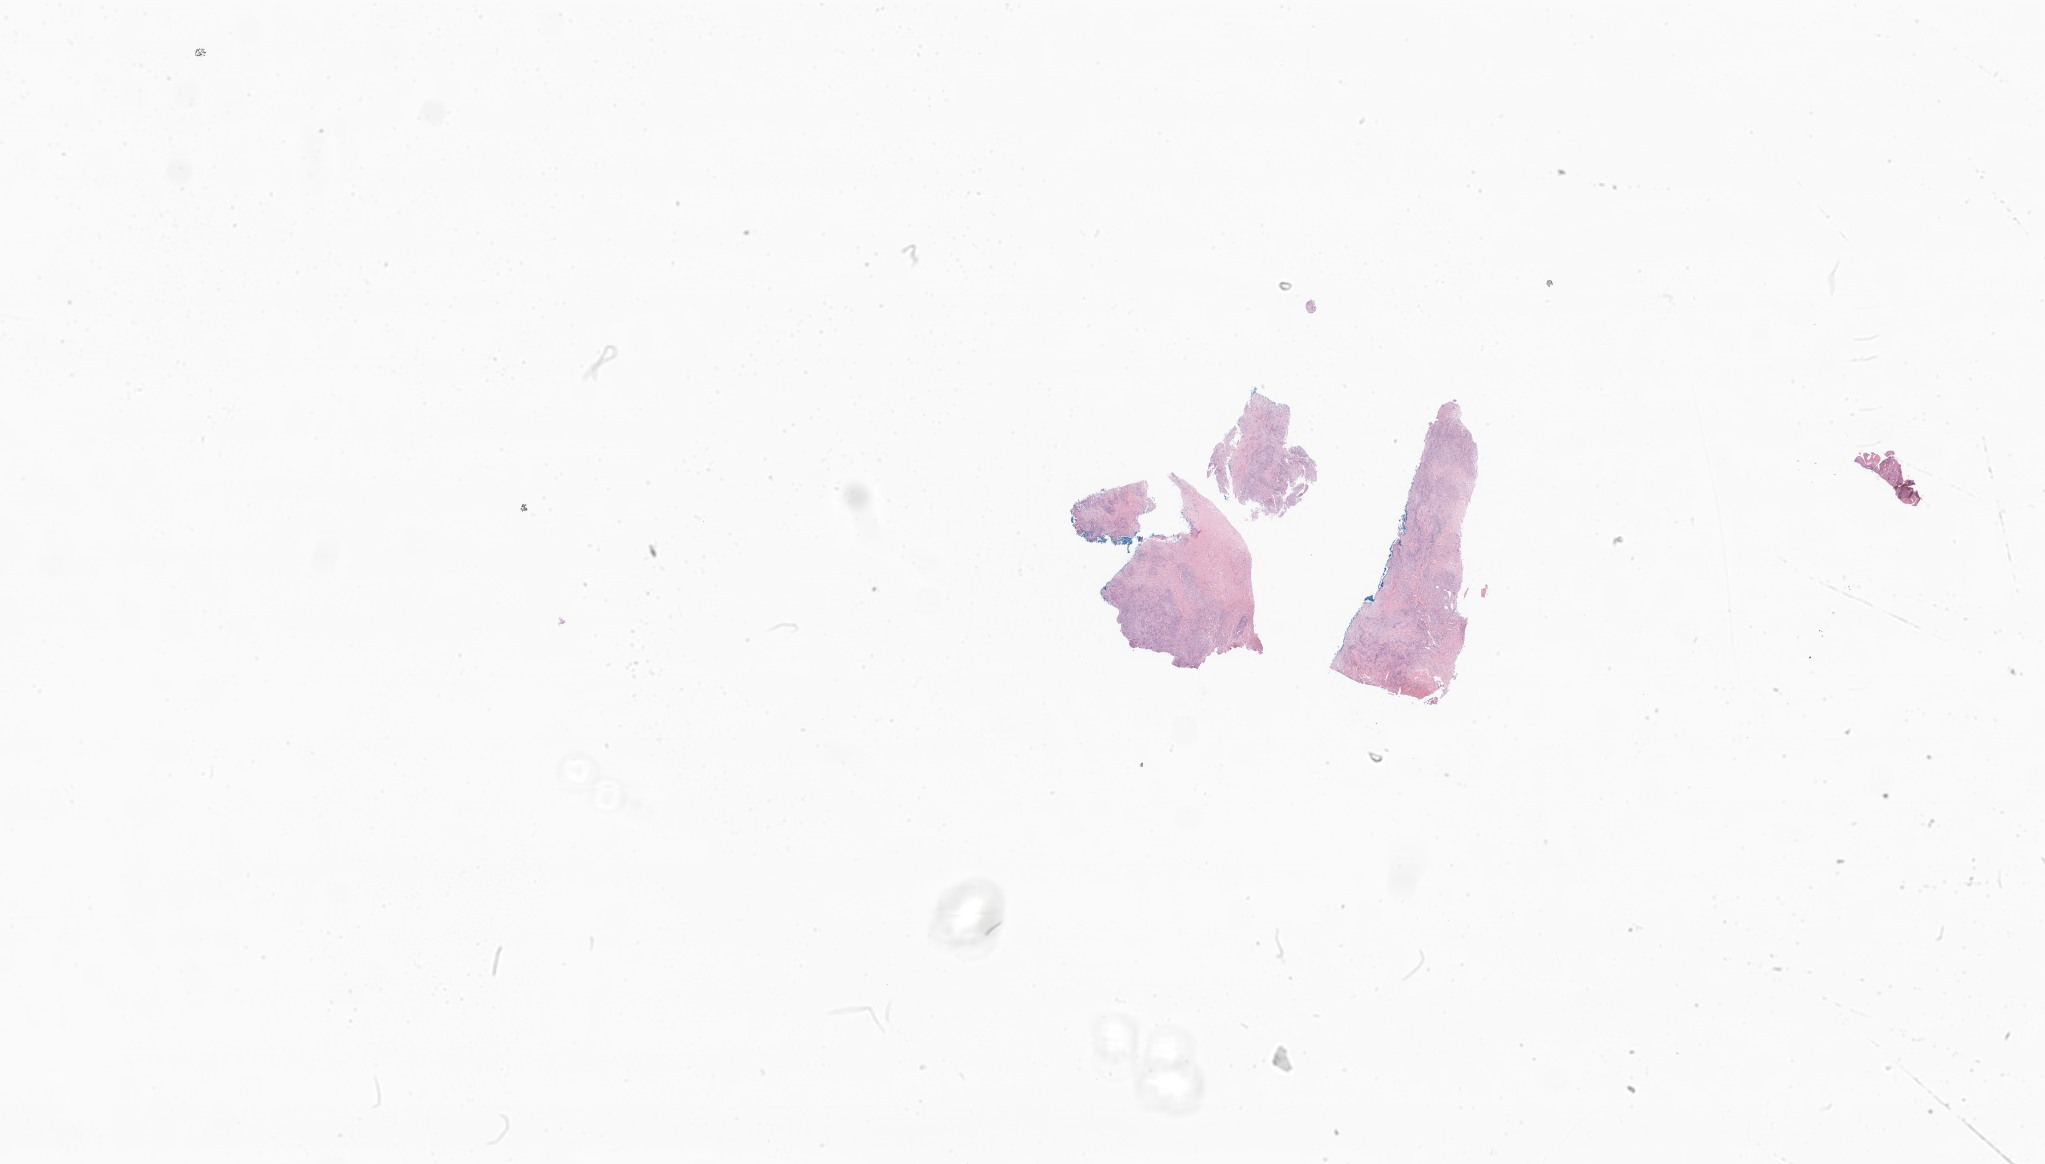
Whole-slide image, H&E stain of tumor tissue from the penis, shown as a low-resolution overview of the whole scanned area (about 34.5 x 19.6 mm); formalin-fixed, paraffin-embedded (FFPE) tissue. Male patient, age 230 months (19 years 2 months).
- diagnosis: Epithelioid sarcoma, NOS